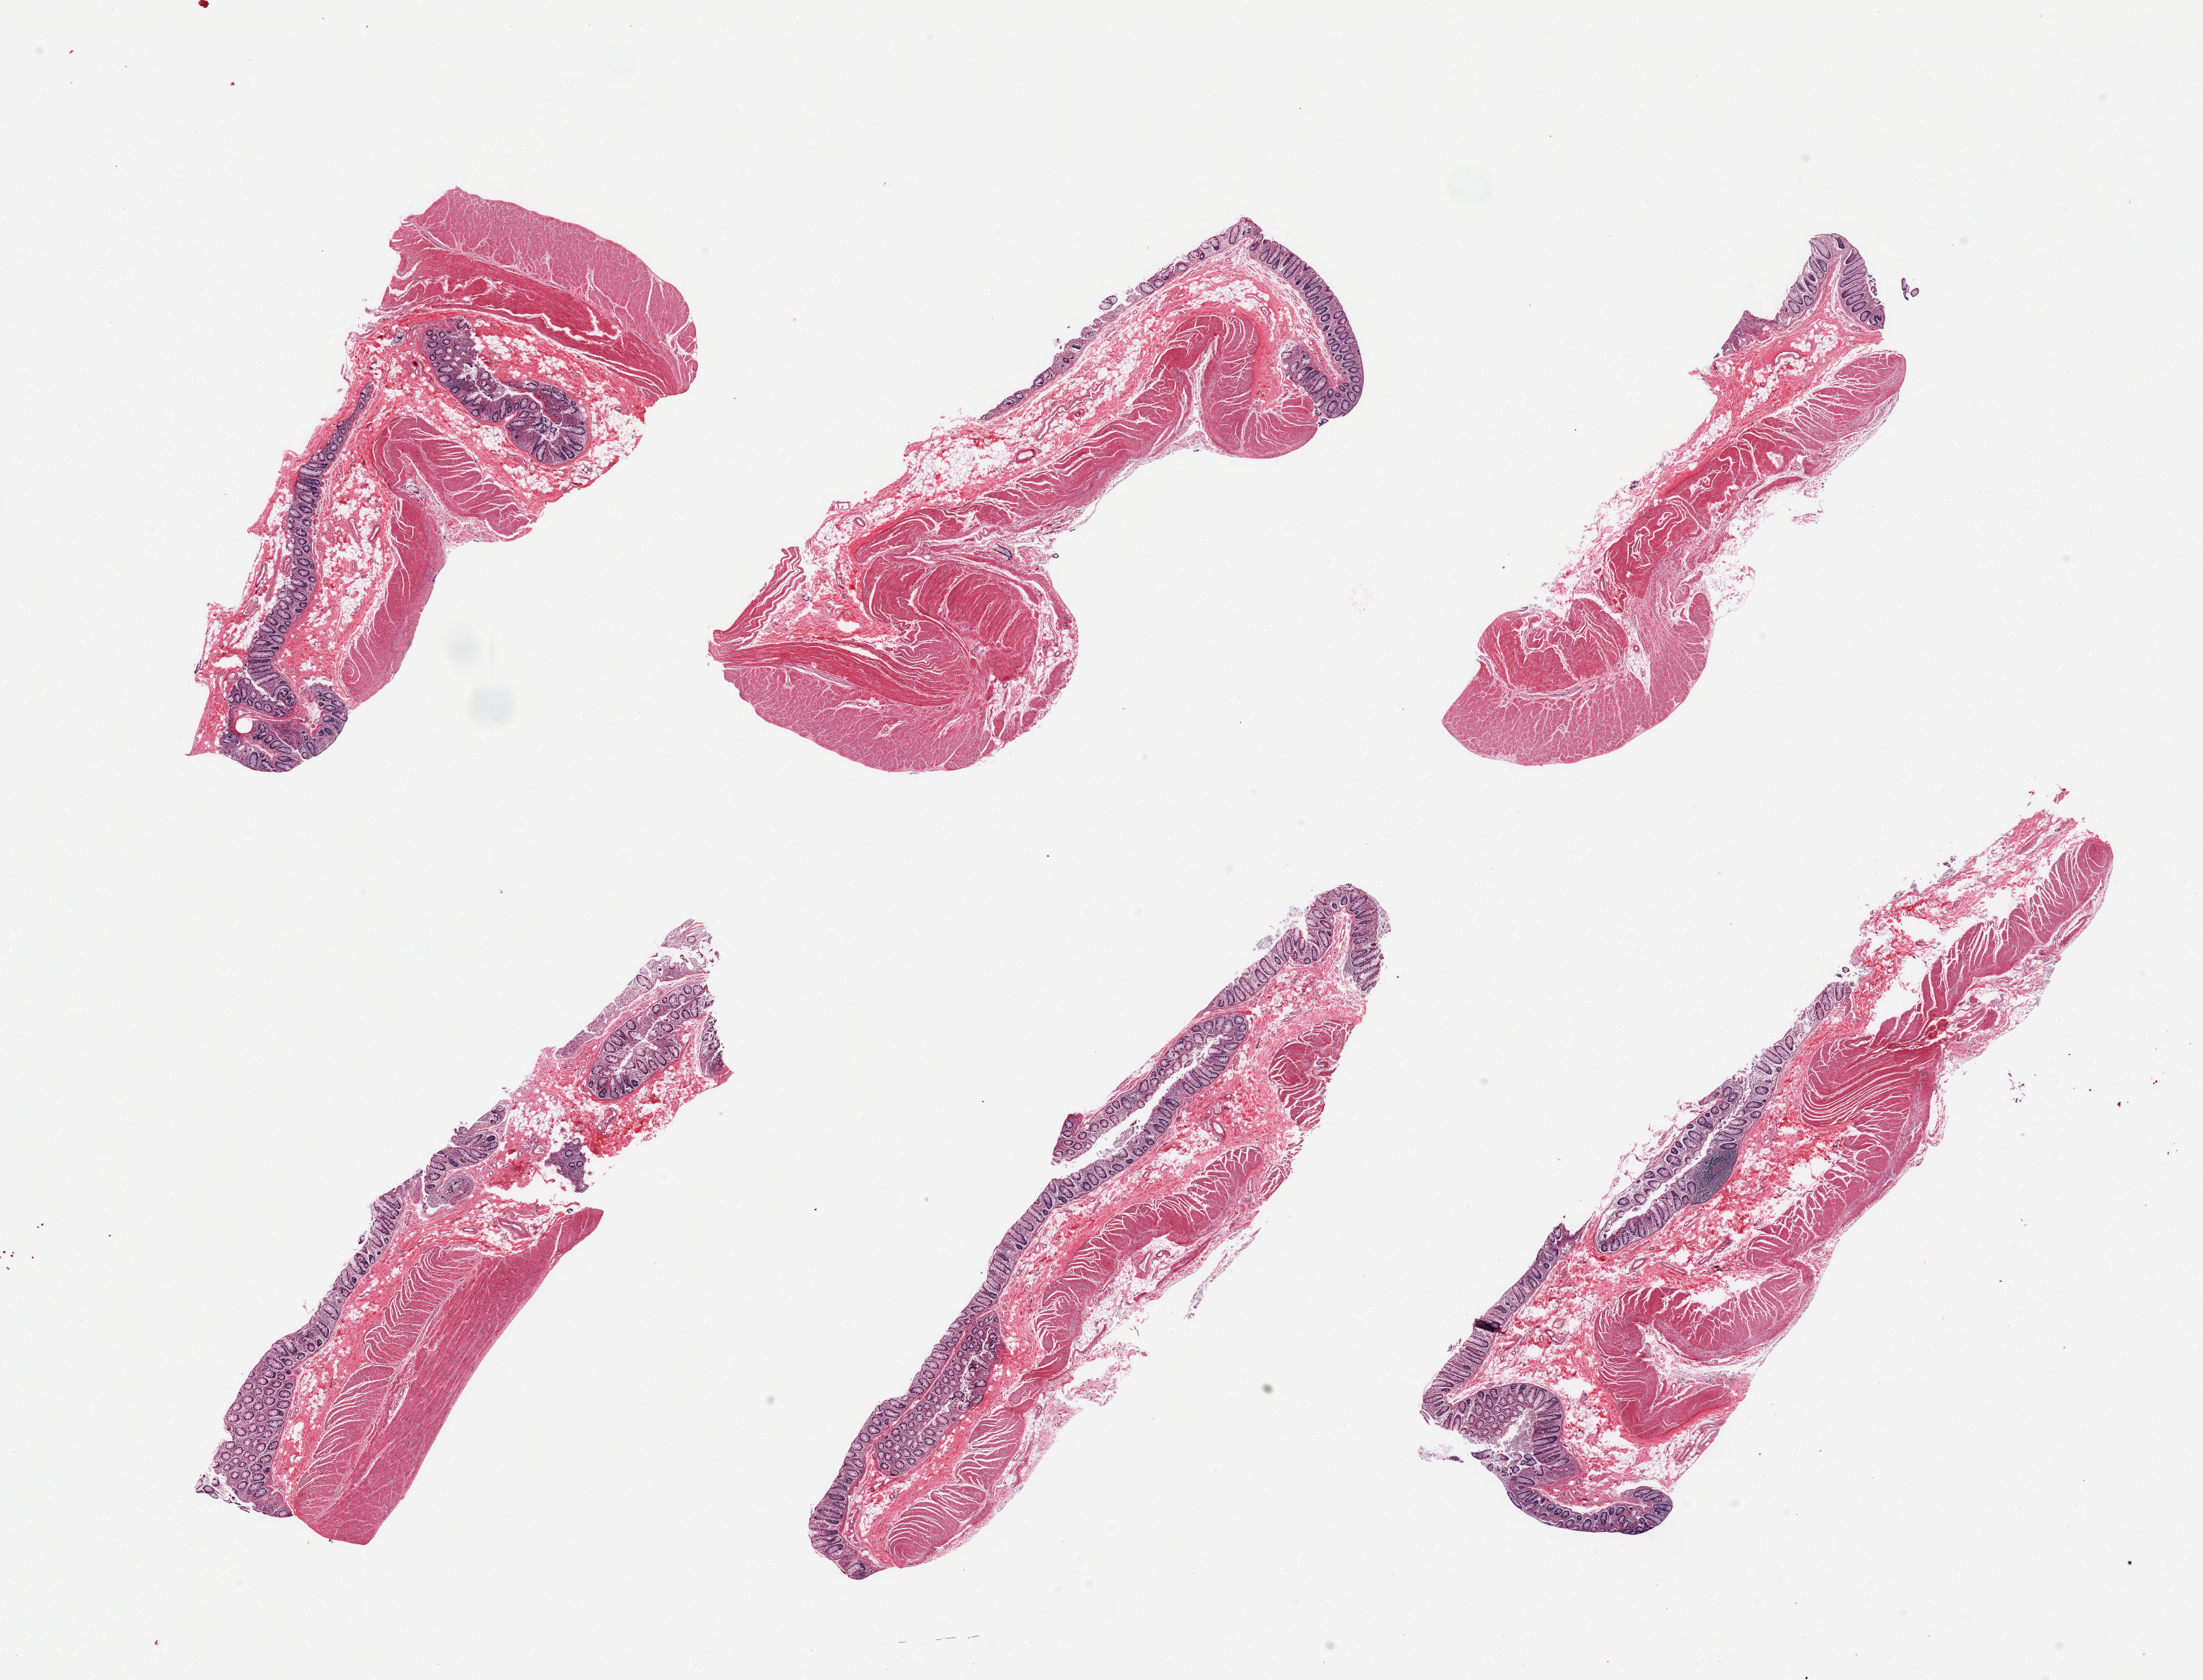
Whole-slide image, hematoxylin and eosin (H&E) stain, low-resolution overview of the scanned area, about 26.6 x 20.3 mm (acquisition: 20x scan). PAXgene-fixed, paraffin-embedded tissue. Target tissue: transverse colon. Donor tissue sample. Male donor.
Review note (as recorded): 6 pieces; variably autolyzed mucosa with some melanosis coli/pigmented macrophages, muscularis also present.